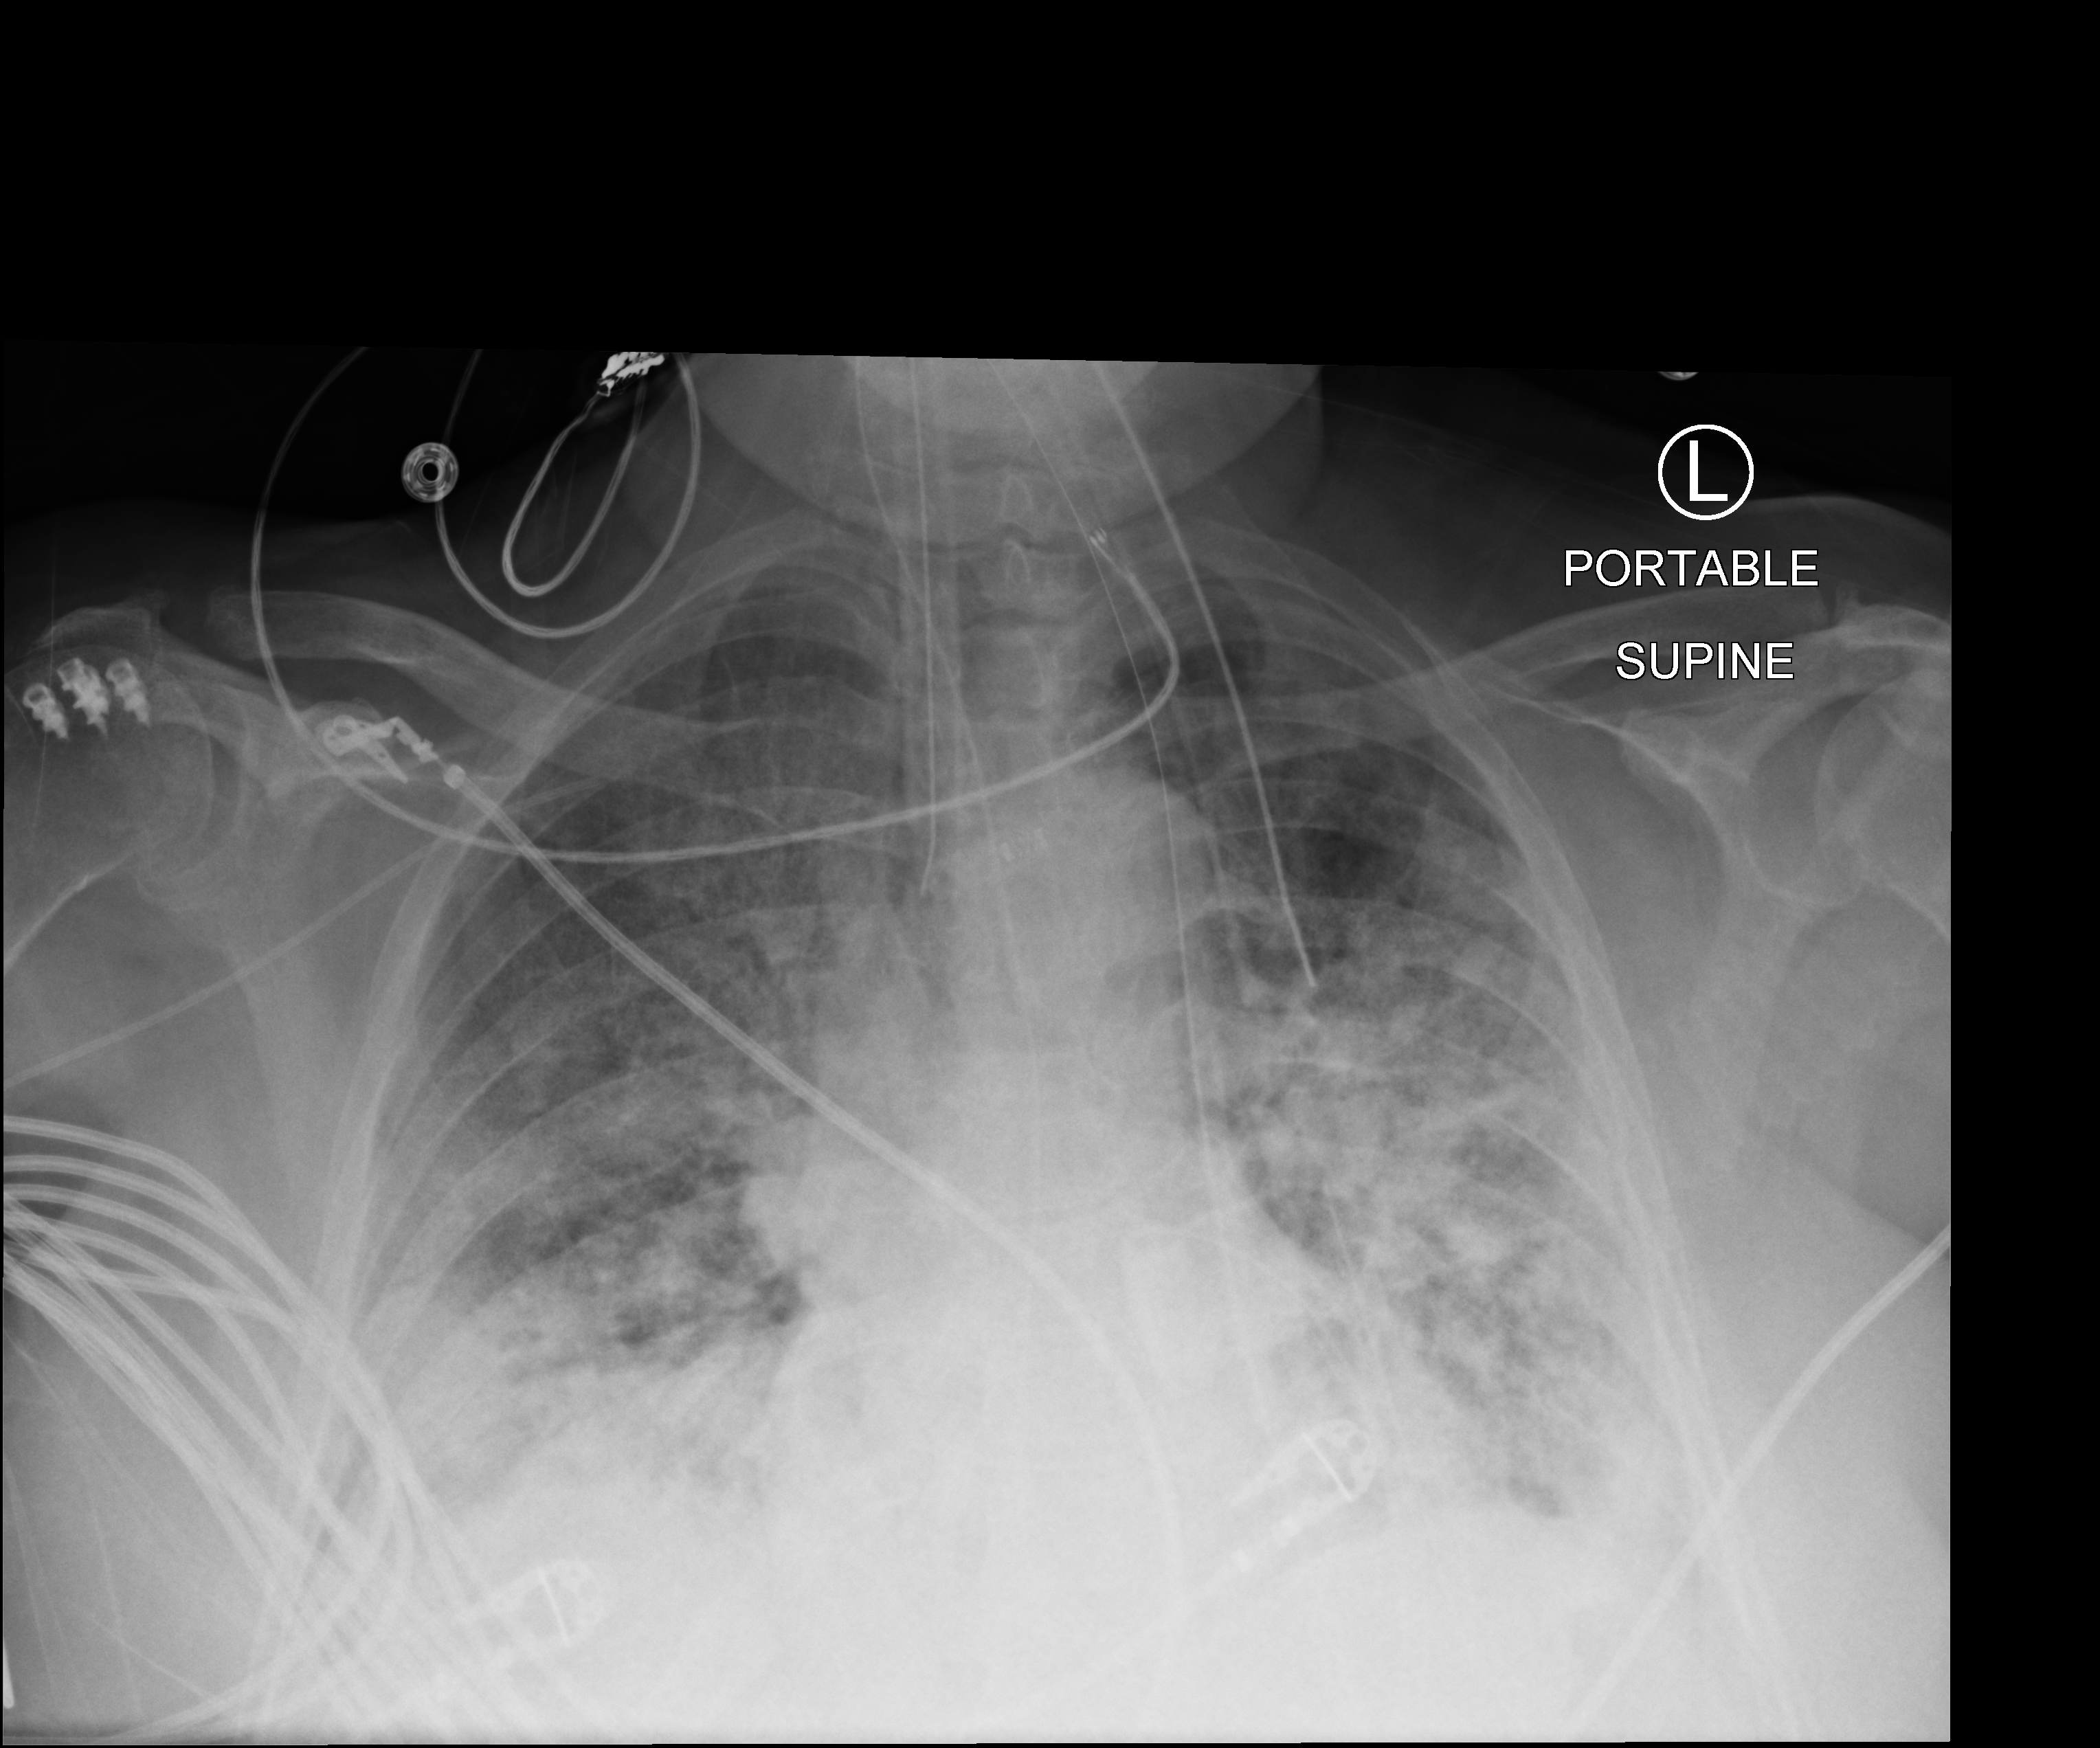
Bedside chest radiograph (computed radiography), anteroposterior (AP) projection. Patient hospitalised with COVID-19; female, aged 60–74 years.
Admission-level facts for this patient (not findings on this image; timing relative to this image not recorded): mechanically ventilated during this hospital stay: yes; admitted to intensive care during this hospital stay: yes; chronic kidney disease (admission record): no.